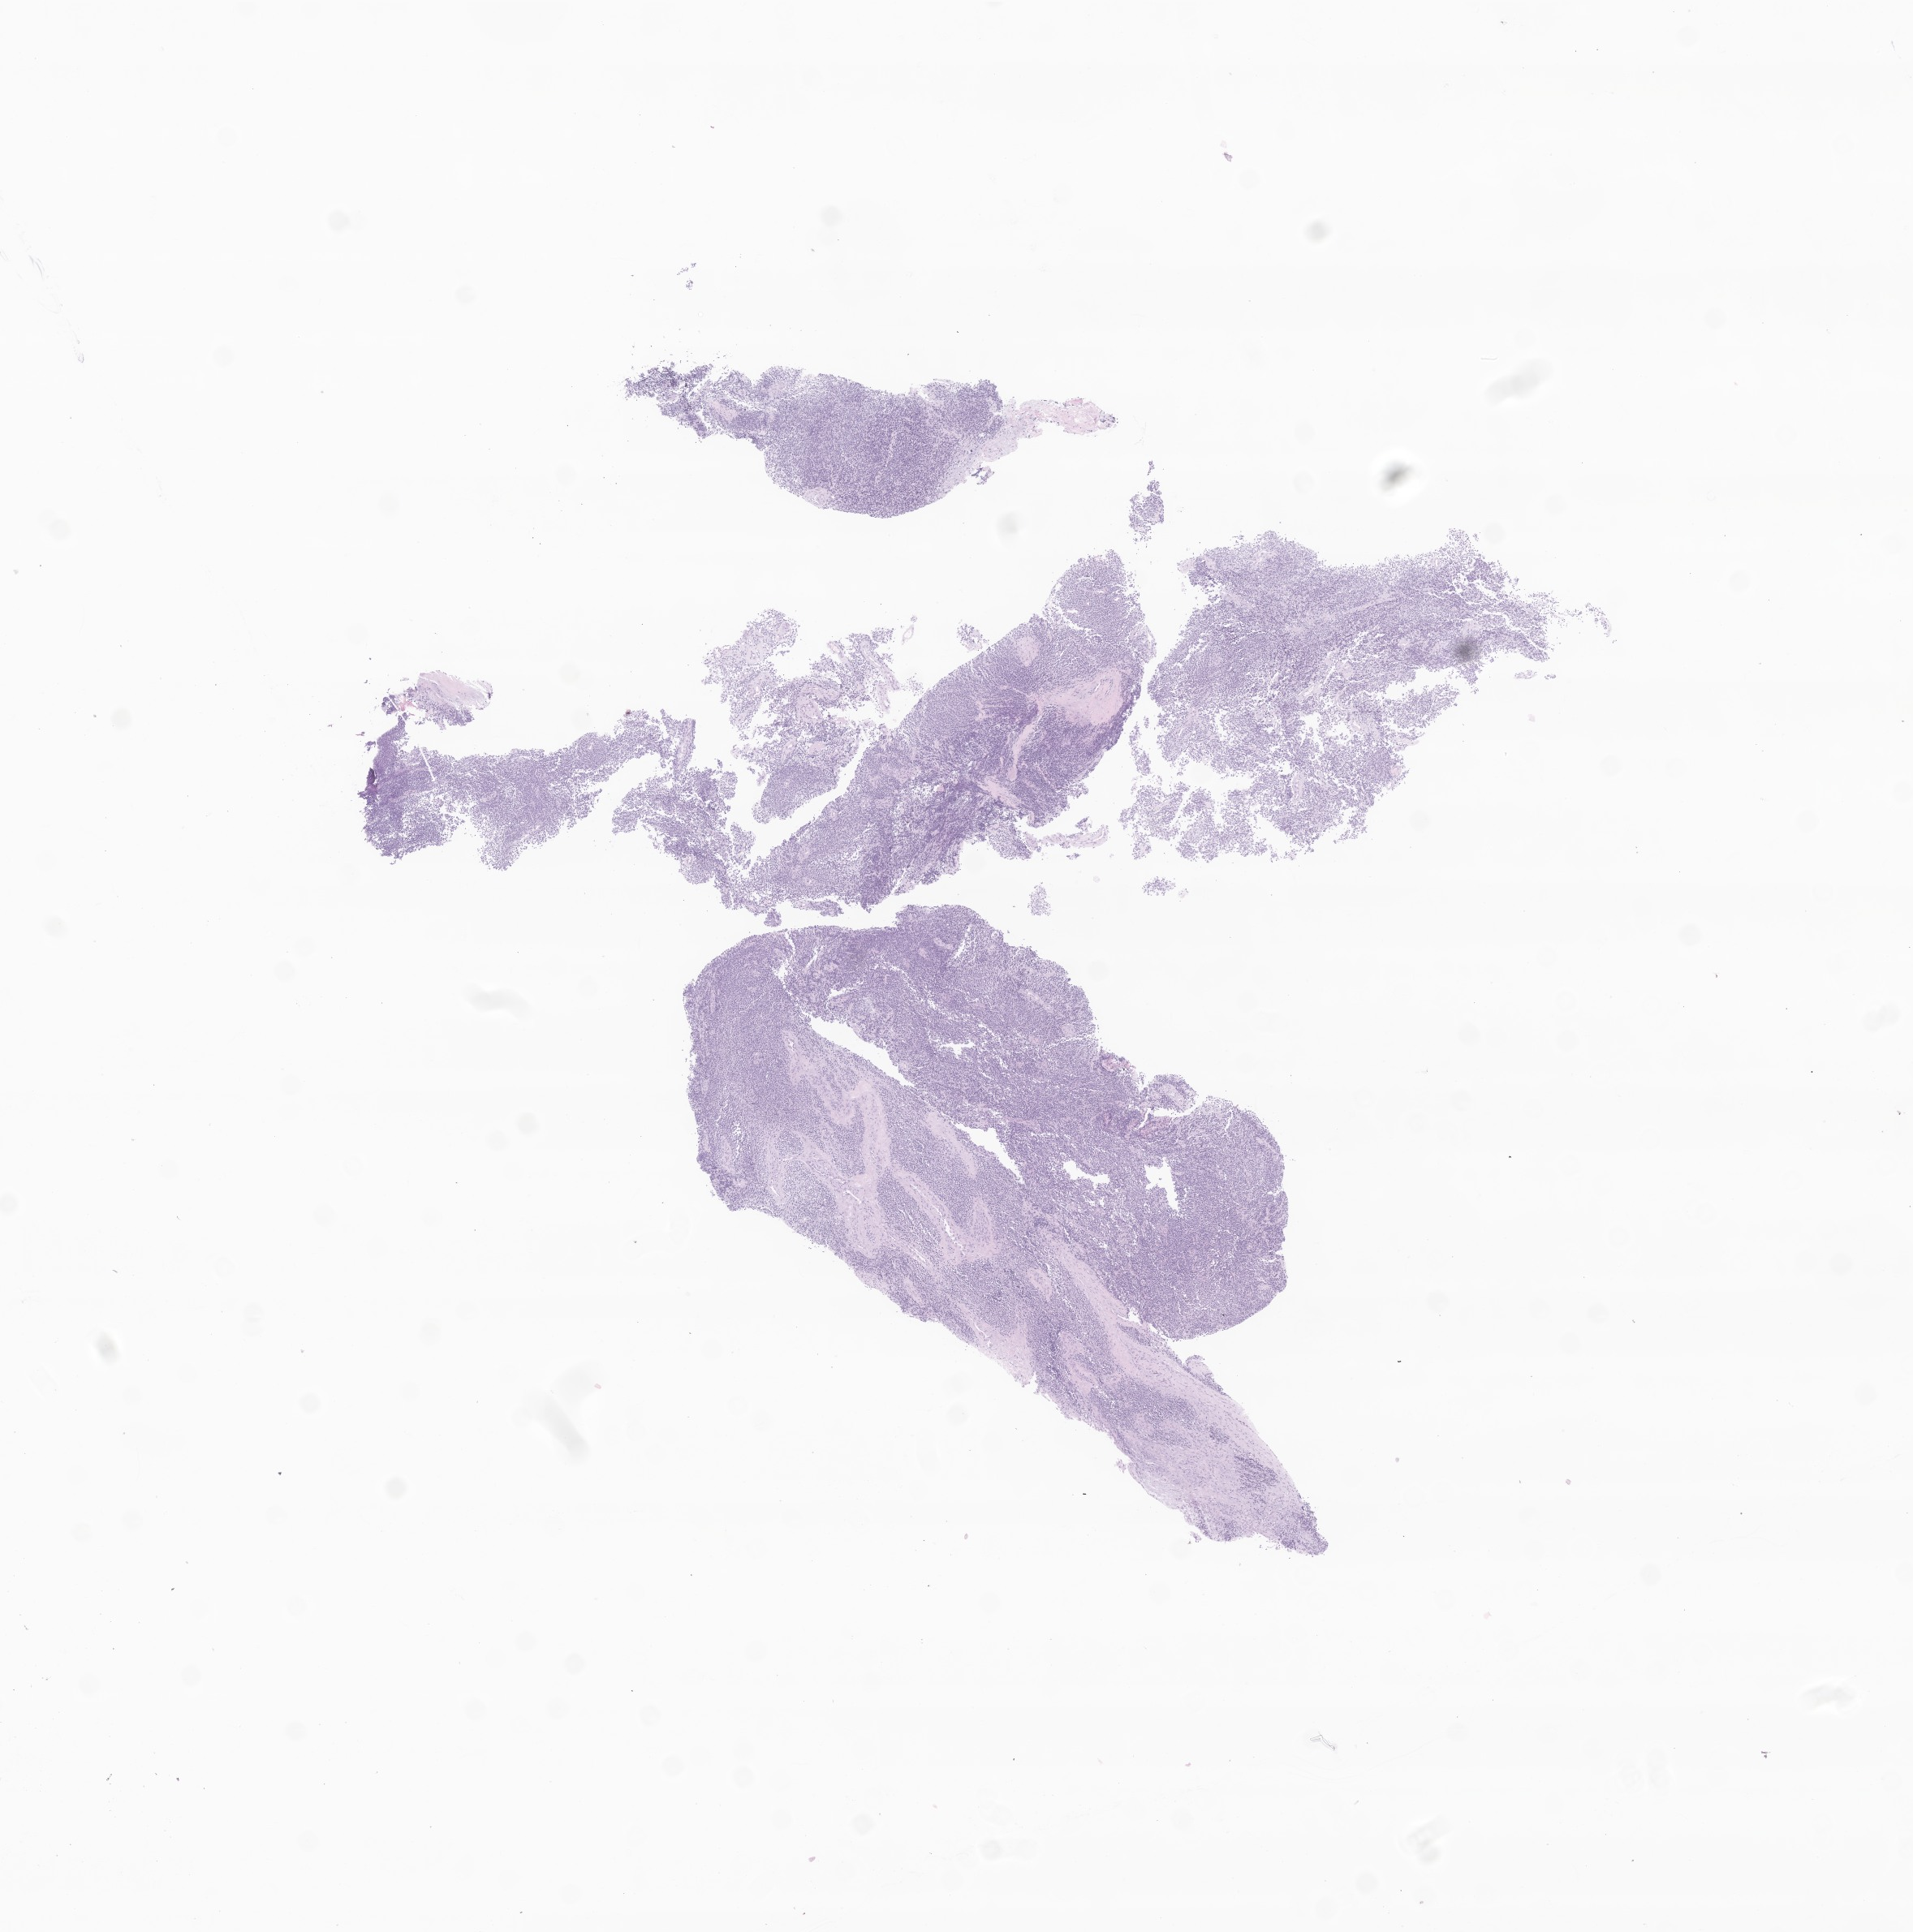
Haematoxylin and eosin whole-slide image of tumor tissue from the abdomen, low-resolution overview of the scanned area, about 9.9 x 10.0 mm; formalin-fixed paraffin-embedded section. Patient: male, age 116 months (9 years 8 months).
Diagnosis: Desmoplastic small round cell tumor.